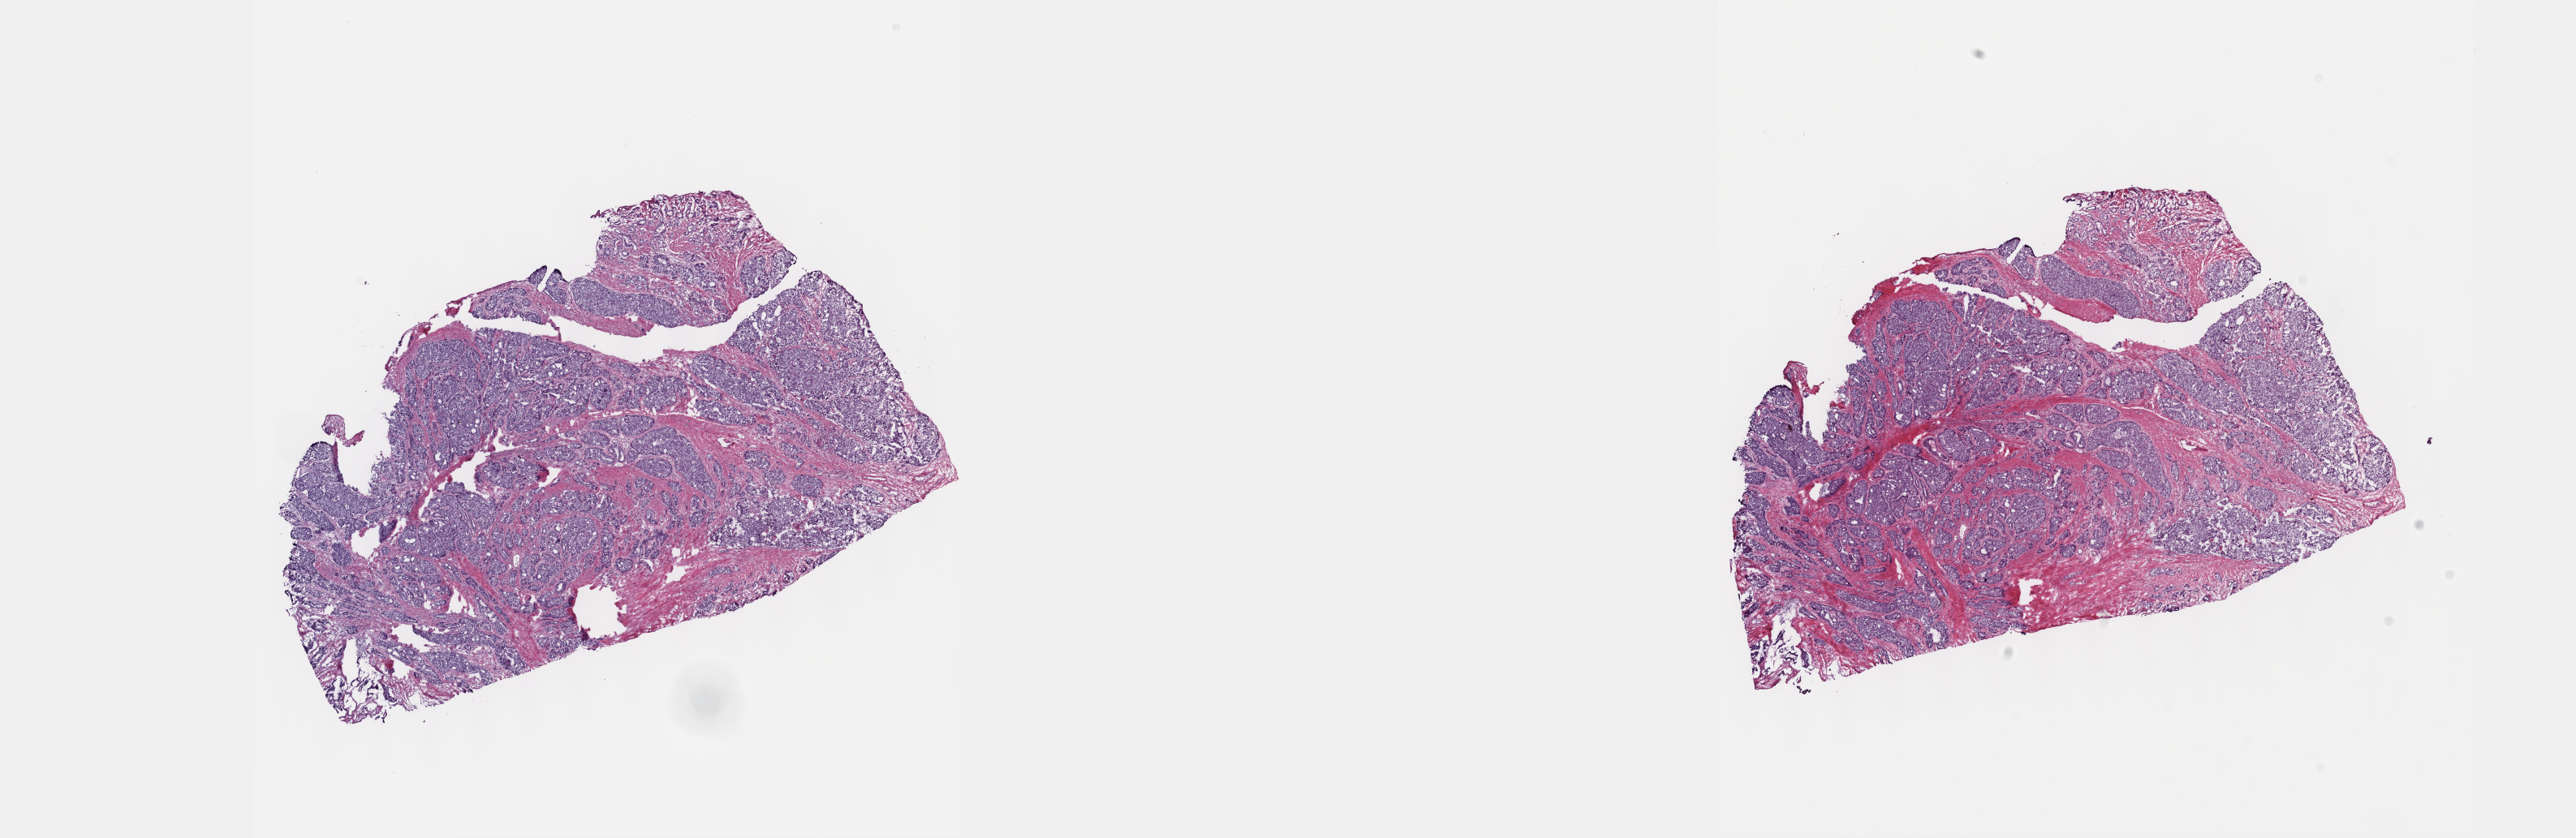
Whole-slide histology image, Hematoxylin and eosin (H&E) stained — whole scanned area (about 25.7 x 8.3 mm, from a 40x scan) shown as a low-resolution overview. Frozen section from the top of the tissue portion. Prostate, primary tumour sample. Male, age 63 years at initial diagnosis. Gleason score: 9 (4+5). Slide review estimates, as recorded: tumour cells 70%, tumour nuclei 70%, normal cells 0%, stromal cells 30%, necrosis 0%. Inflammatory infiltration, as recorded: lymphocyte infiltration 40%, monocyte infiltration 20%, neutrophil infiltration 20%.
Pathologic diagnosis: Adenocarcinoma, NOS (prostate gland). Lymph nodes positive (case pathology): 1 of 15 examined.